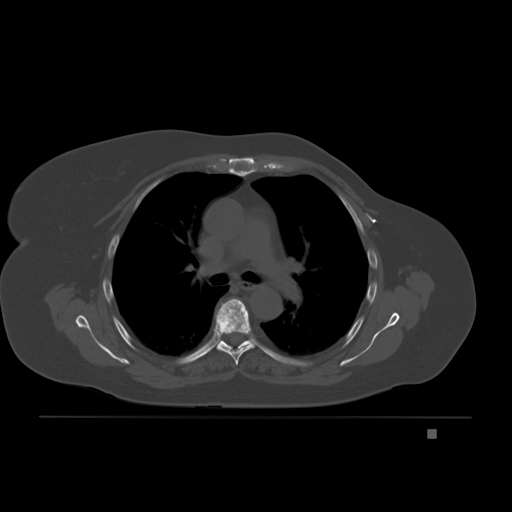
CT including the spine, one axial slice. Position 142 of 221 along the scan axis. Bone window (W 1800 / L 400 HU). 3 mm slice thickness. 512 × 512 image matrix, field of view 474 × 474 mm. Patient: female, 63 years. Case-level facts recorded for this patient, not image findings: primary cancer: breast.
Structures marked on this image (semi-automatically segmented with operator editing):
- T5 vertebra: box from (x=215, y=298) to (x=256, y=365) px
- T6 vertebra: (x=218, y=339)–(x=250, y=349)